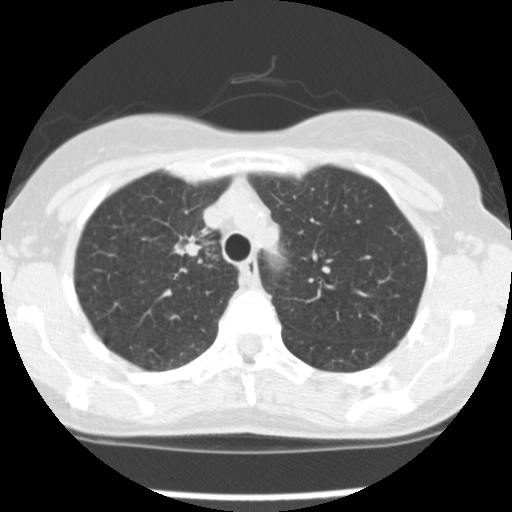
Axial slice from a low-dose chest CT screening exam; baseline screening round; lung window (W 1500 / L -600 HU); standard (soft-tissue) reconstruction kernel (STANDARD); 512 × 512 image matrix, field of view 282 × 282 mm. Female, age 57 years at enrolment. Current smoker at enrolment.
- Expert-annotated lung lesion, bounding box (x1, y1, x2, y2) in pixels: (165, 228, 217, 274).
- The exam's reader record, not a measurement of the box and not confirmed to be the same lesion: non-calcified nodule or mass ≥4 mm, left upper lobe, 7 × 6 mm, poorly defined margins, ground glass attenuation.
- Note: the box lies in the patient's right hemithorax on this image, whereas the reader's record names the left lung; they may be different findings.